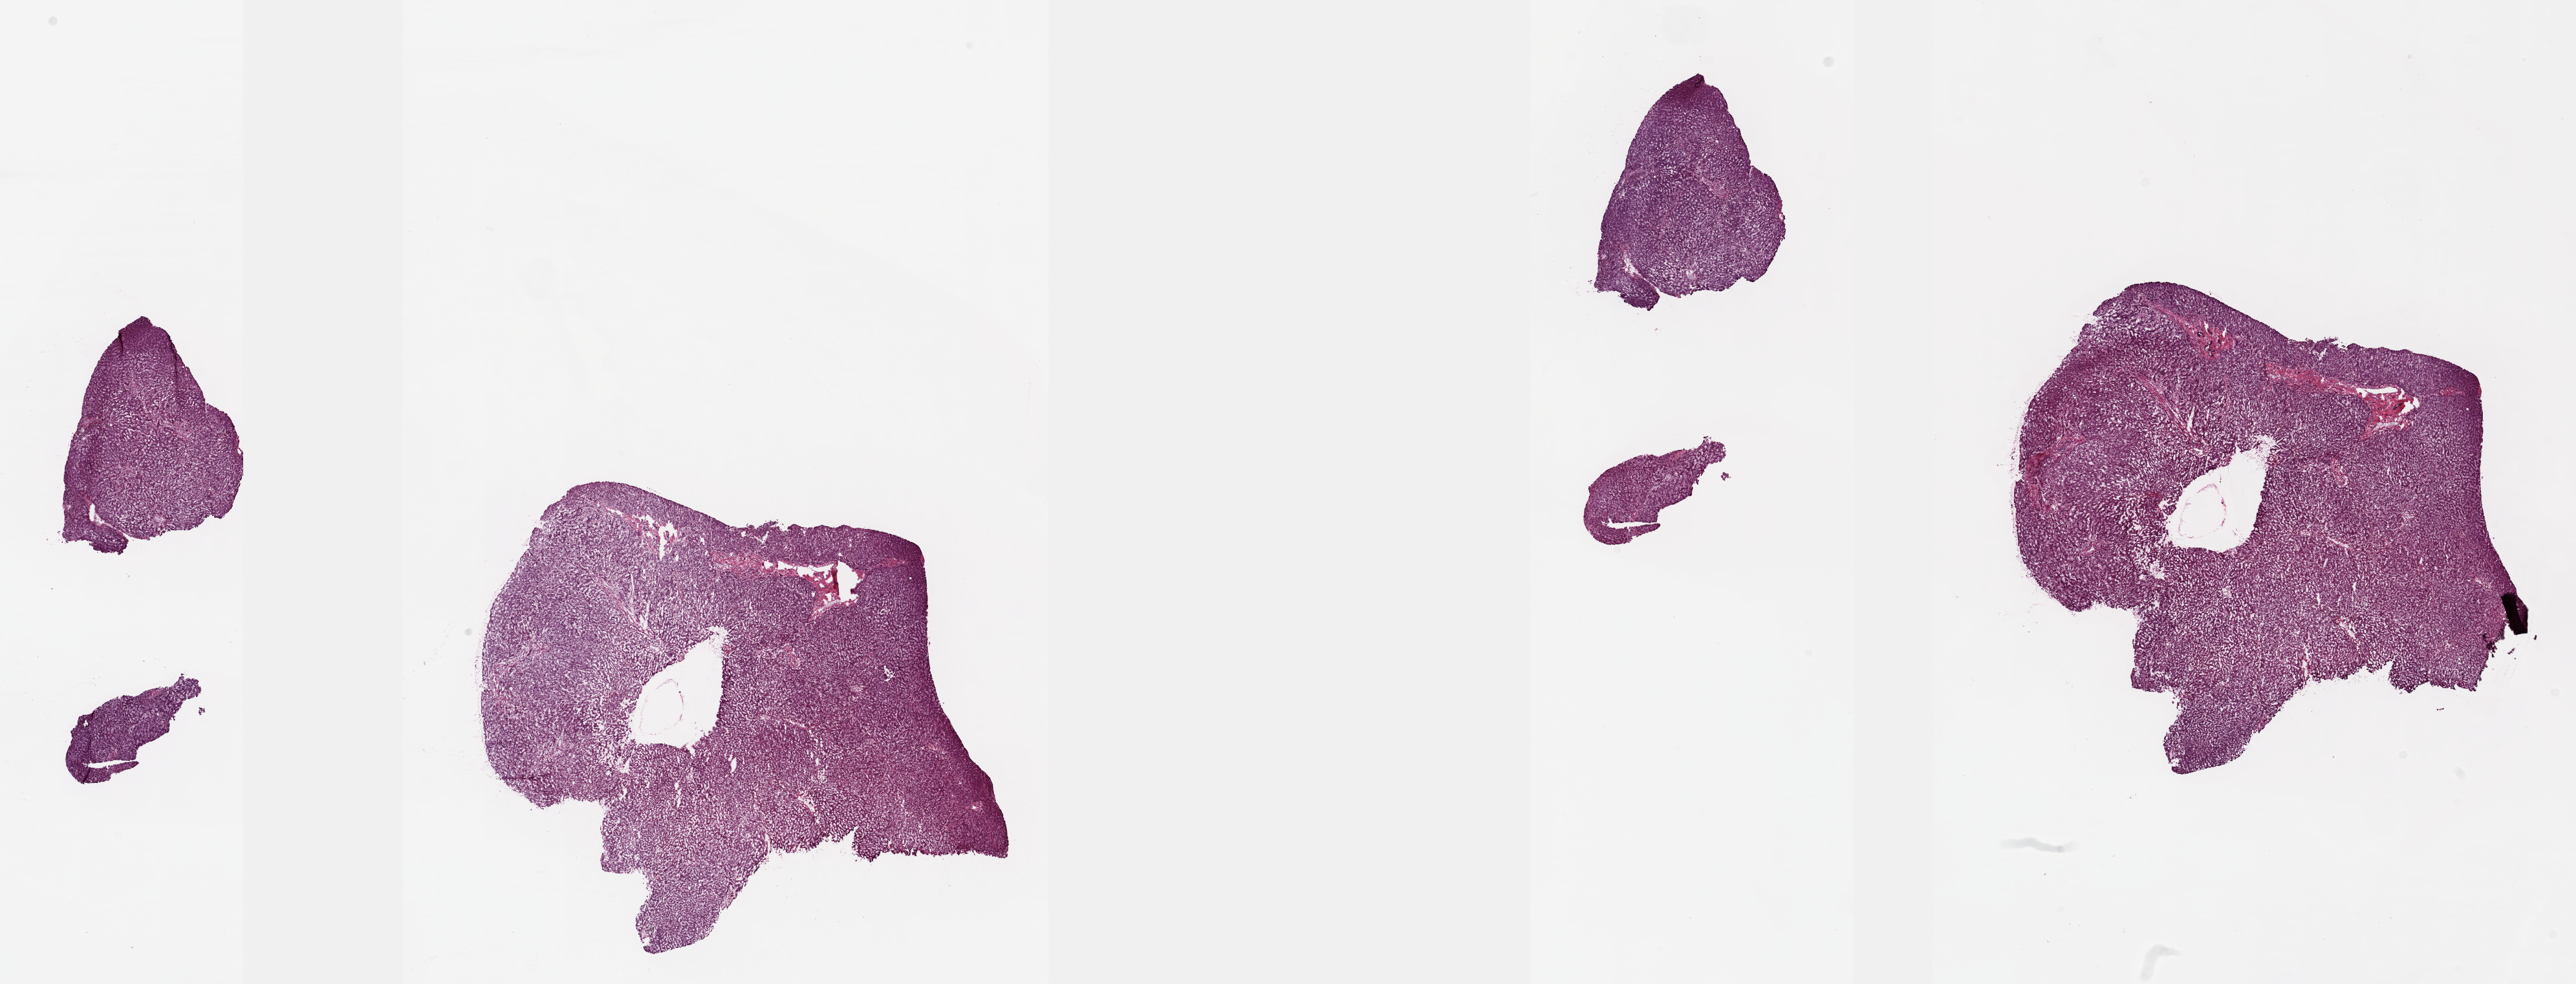
Digitized Hematoxylin and eosin (H&E) stained tissue section (whole slide) — shown as a low-resolution overview of the whole scanned area (about 32.1 x 12.3 mm), frozen section from the top of the tissue portion, sample: solid tissue normal (non-tumour tissue), bile duct. Patient: female, age at initial diagnosis 71 years. Slide review estimates, as recorded: tumour cells 0%, tumour nuclei 0%, normal cells 90%, stromal cells 10%, necrosis 0%. Infiltration values recorded for this section: lymphocyte infiltration 6%, monocyte infiltration 0%, neutrophil infiltration 0%.
This section: solid tissue normal (non-tumour) sample from the same patient. Patient diagnosis: Cholangiocarcinoma (intrahepatic bile duct).